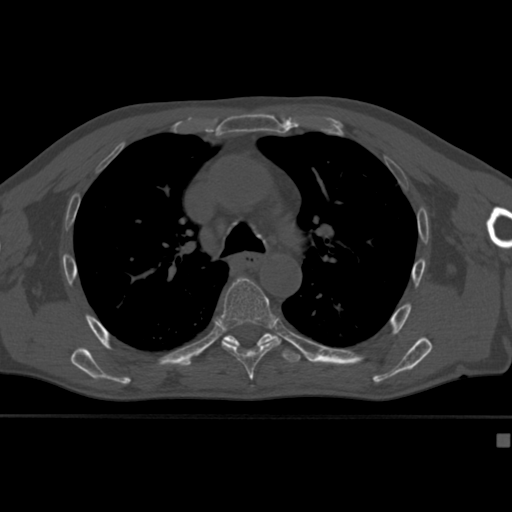
CT including the spine, one axial slice; position 291 of 430 along the scan axis; reconstruction kernel Br40s; 120 kVp; bone window (W 1800 / L 400 HU); 1.5 mm slice thickness; 512 × 512 image matrix, field of view 337 × 337 mm. Male patient, age 64 years. From the clinical record (not read from this slice): primary cancer: uterus.
Outlined on this slice (semi-automatic segmentation, software-assisted and operator-edited):
- T6 vertebra: bounding box <218,277,281,382> (left, top, right, bottom; pixels)
- T7 vertebra: <205,333,301,364>